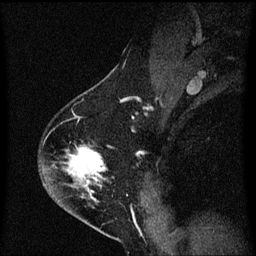
Breast MRI (dynamic contrast-enhanced), one sagittal slice. Dynamic contrast-enhanced series, image 2 of 3 at this slice position (ordered by acquisition). 1.5 T. TE 4.2 ms, TR 8.4 ms. 2 mm slice thickness. 256 × 256 image matrix. Female patient, age 54 years. Case-level facts recorded for this patient, not image findings: setting: breast cancer imaged before/during neoadjuvant chemotherapy; receptor status: HER2-positive.
Outlined on this slice (semi-automatically segmented with operator editing):
- analysis volume of interest (the breast-tissue region the enhancement analysis was run in; not a lesion): bounding box [x1, y1, x2, y2] px = [44, 146, 109, 213]
- tumour enhancement mask (voxels above the 70 % enhancement threshold inside the analysis volume of interest): [68, 148, 105, 183]